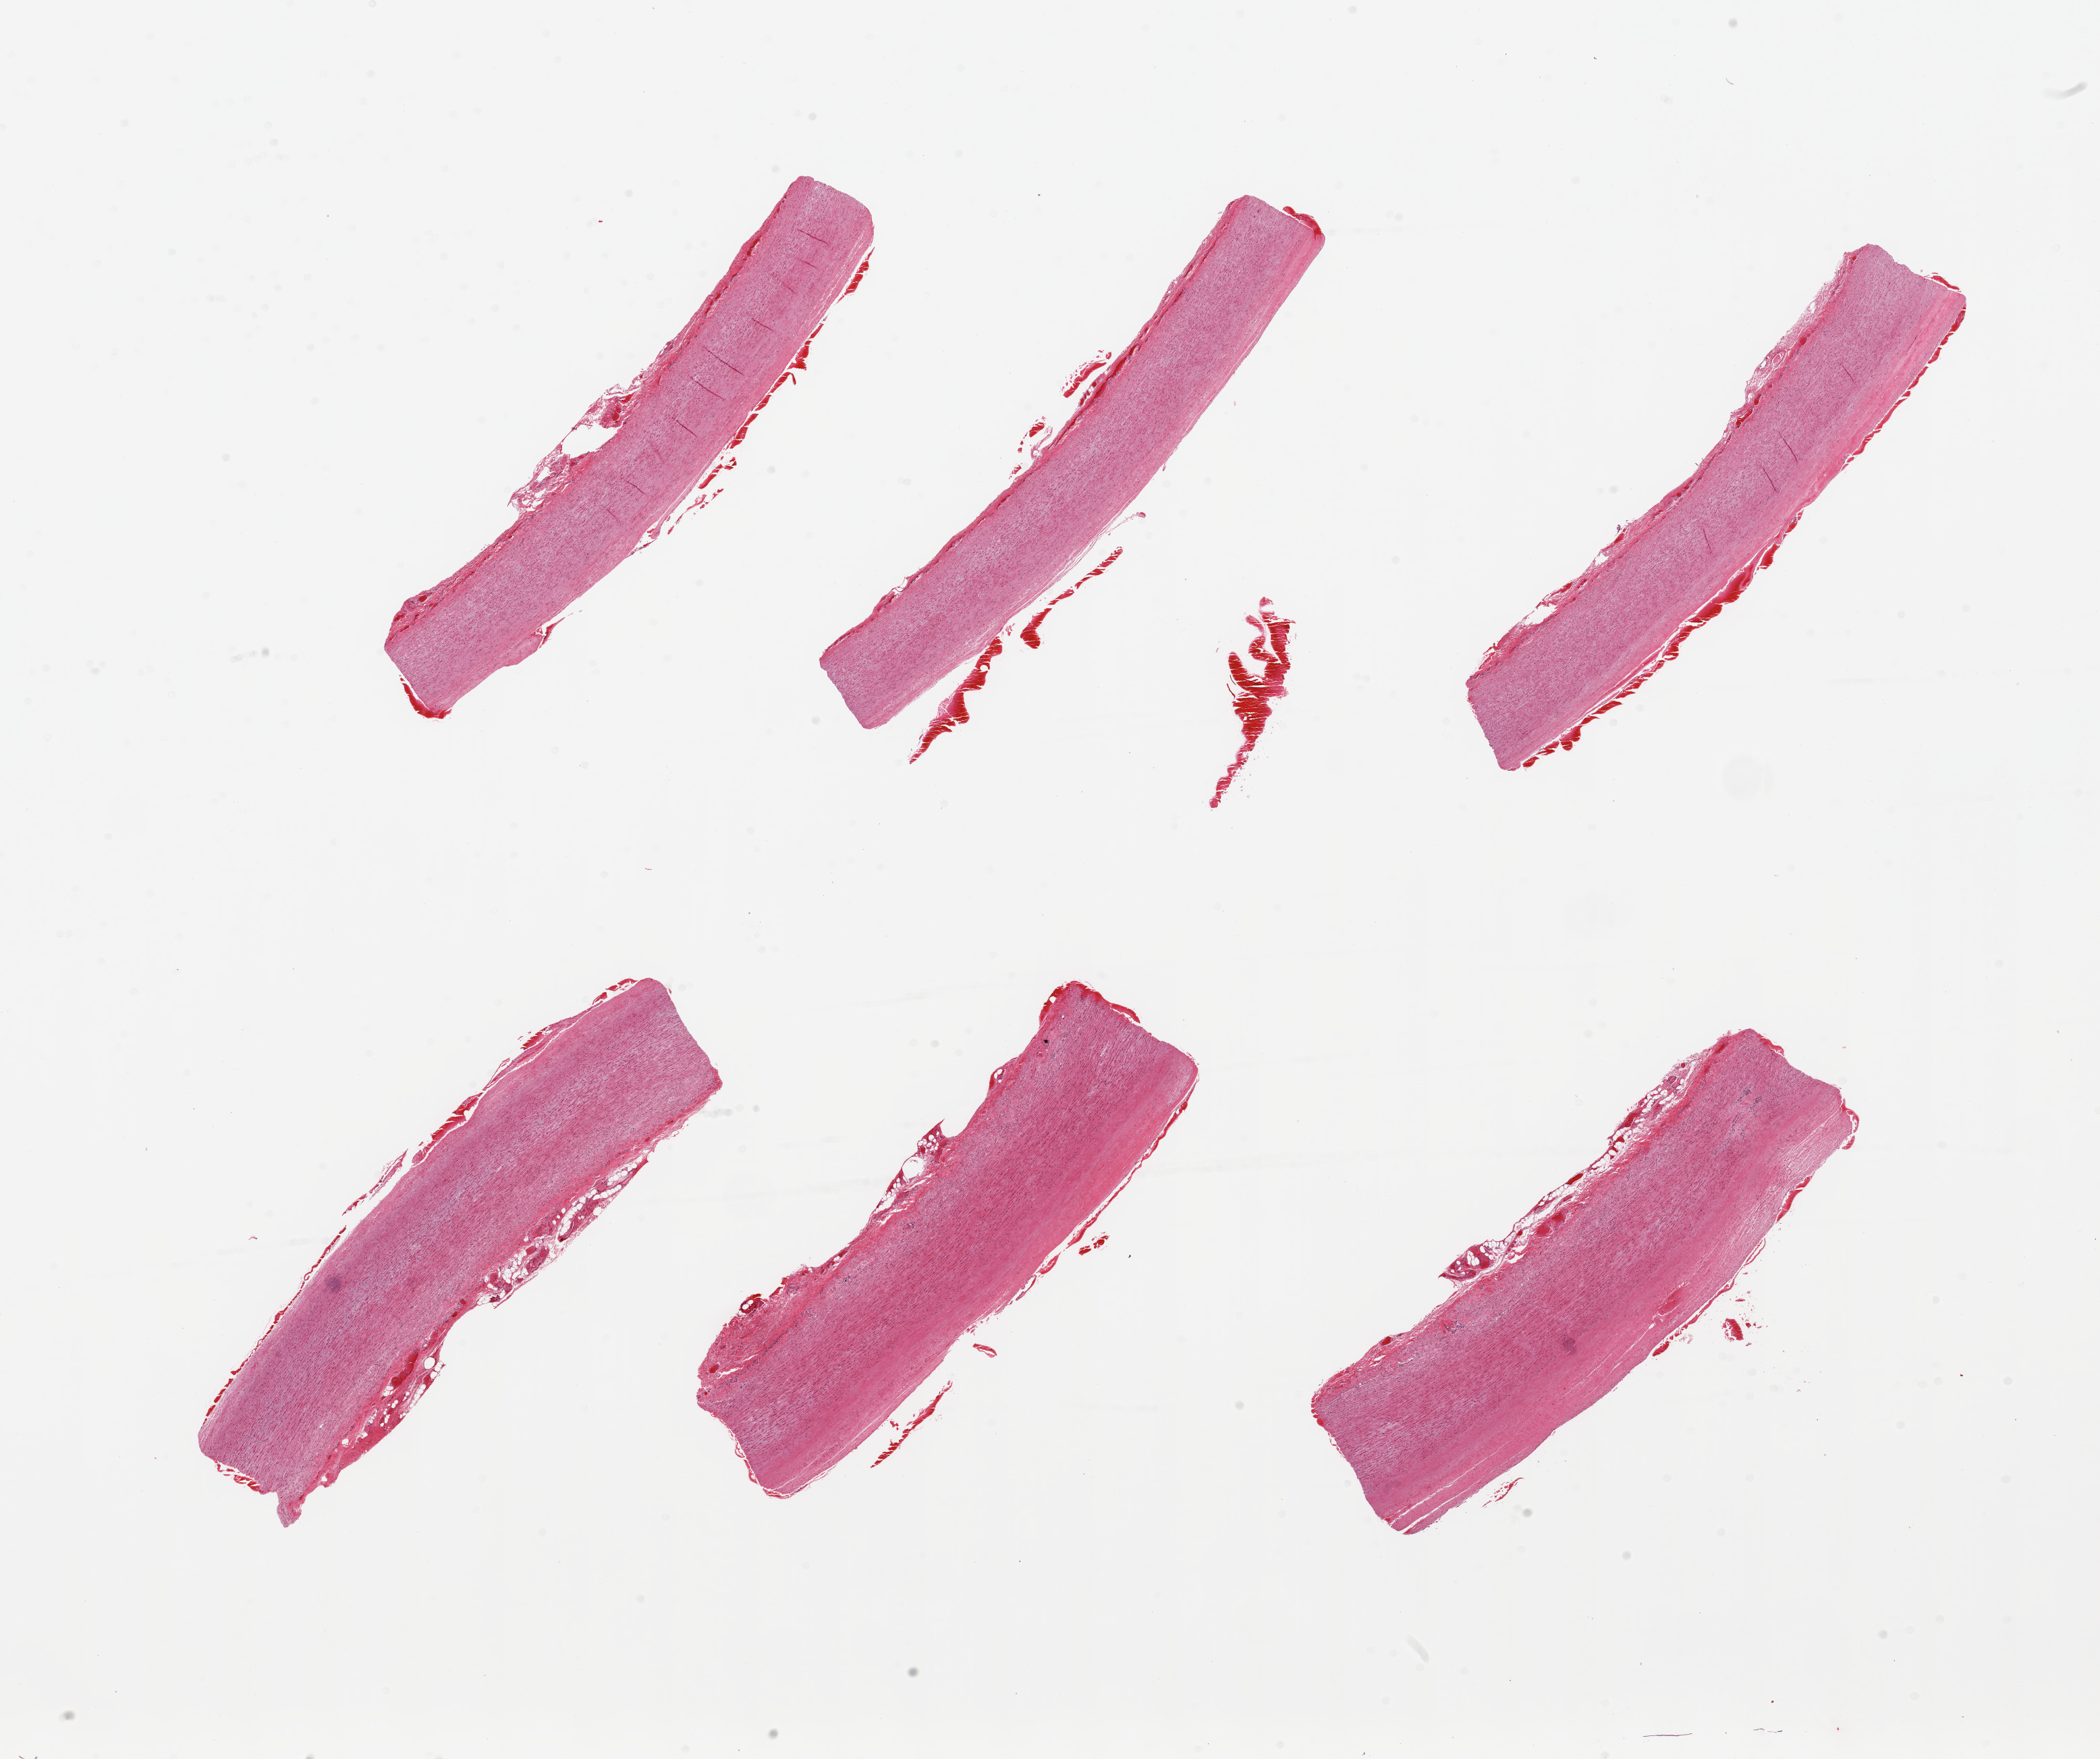
Whole-slide image, H&E stain, shown as a low-resolution overview of the whole scanned area (about 24.6 x 20.6 mm); PAXgene-fixed paraffin-embedded (PFPE) section; sampled site (target tissue): aorta; tissue donor sample.
- reviewer comment on this tissue sample: 6 pieces; atherosclerosis